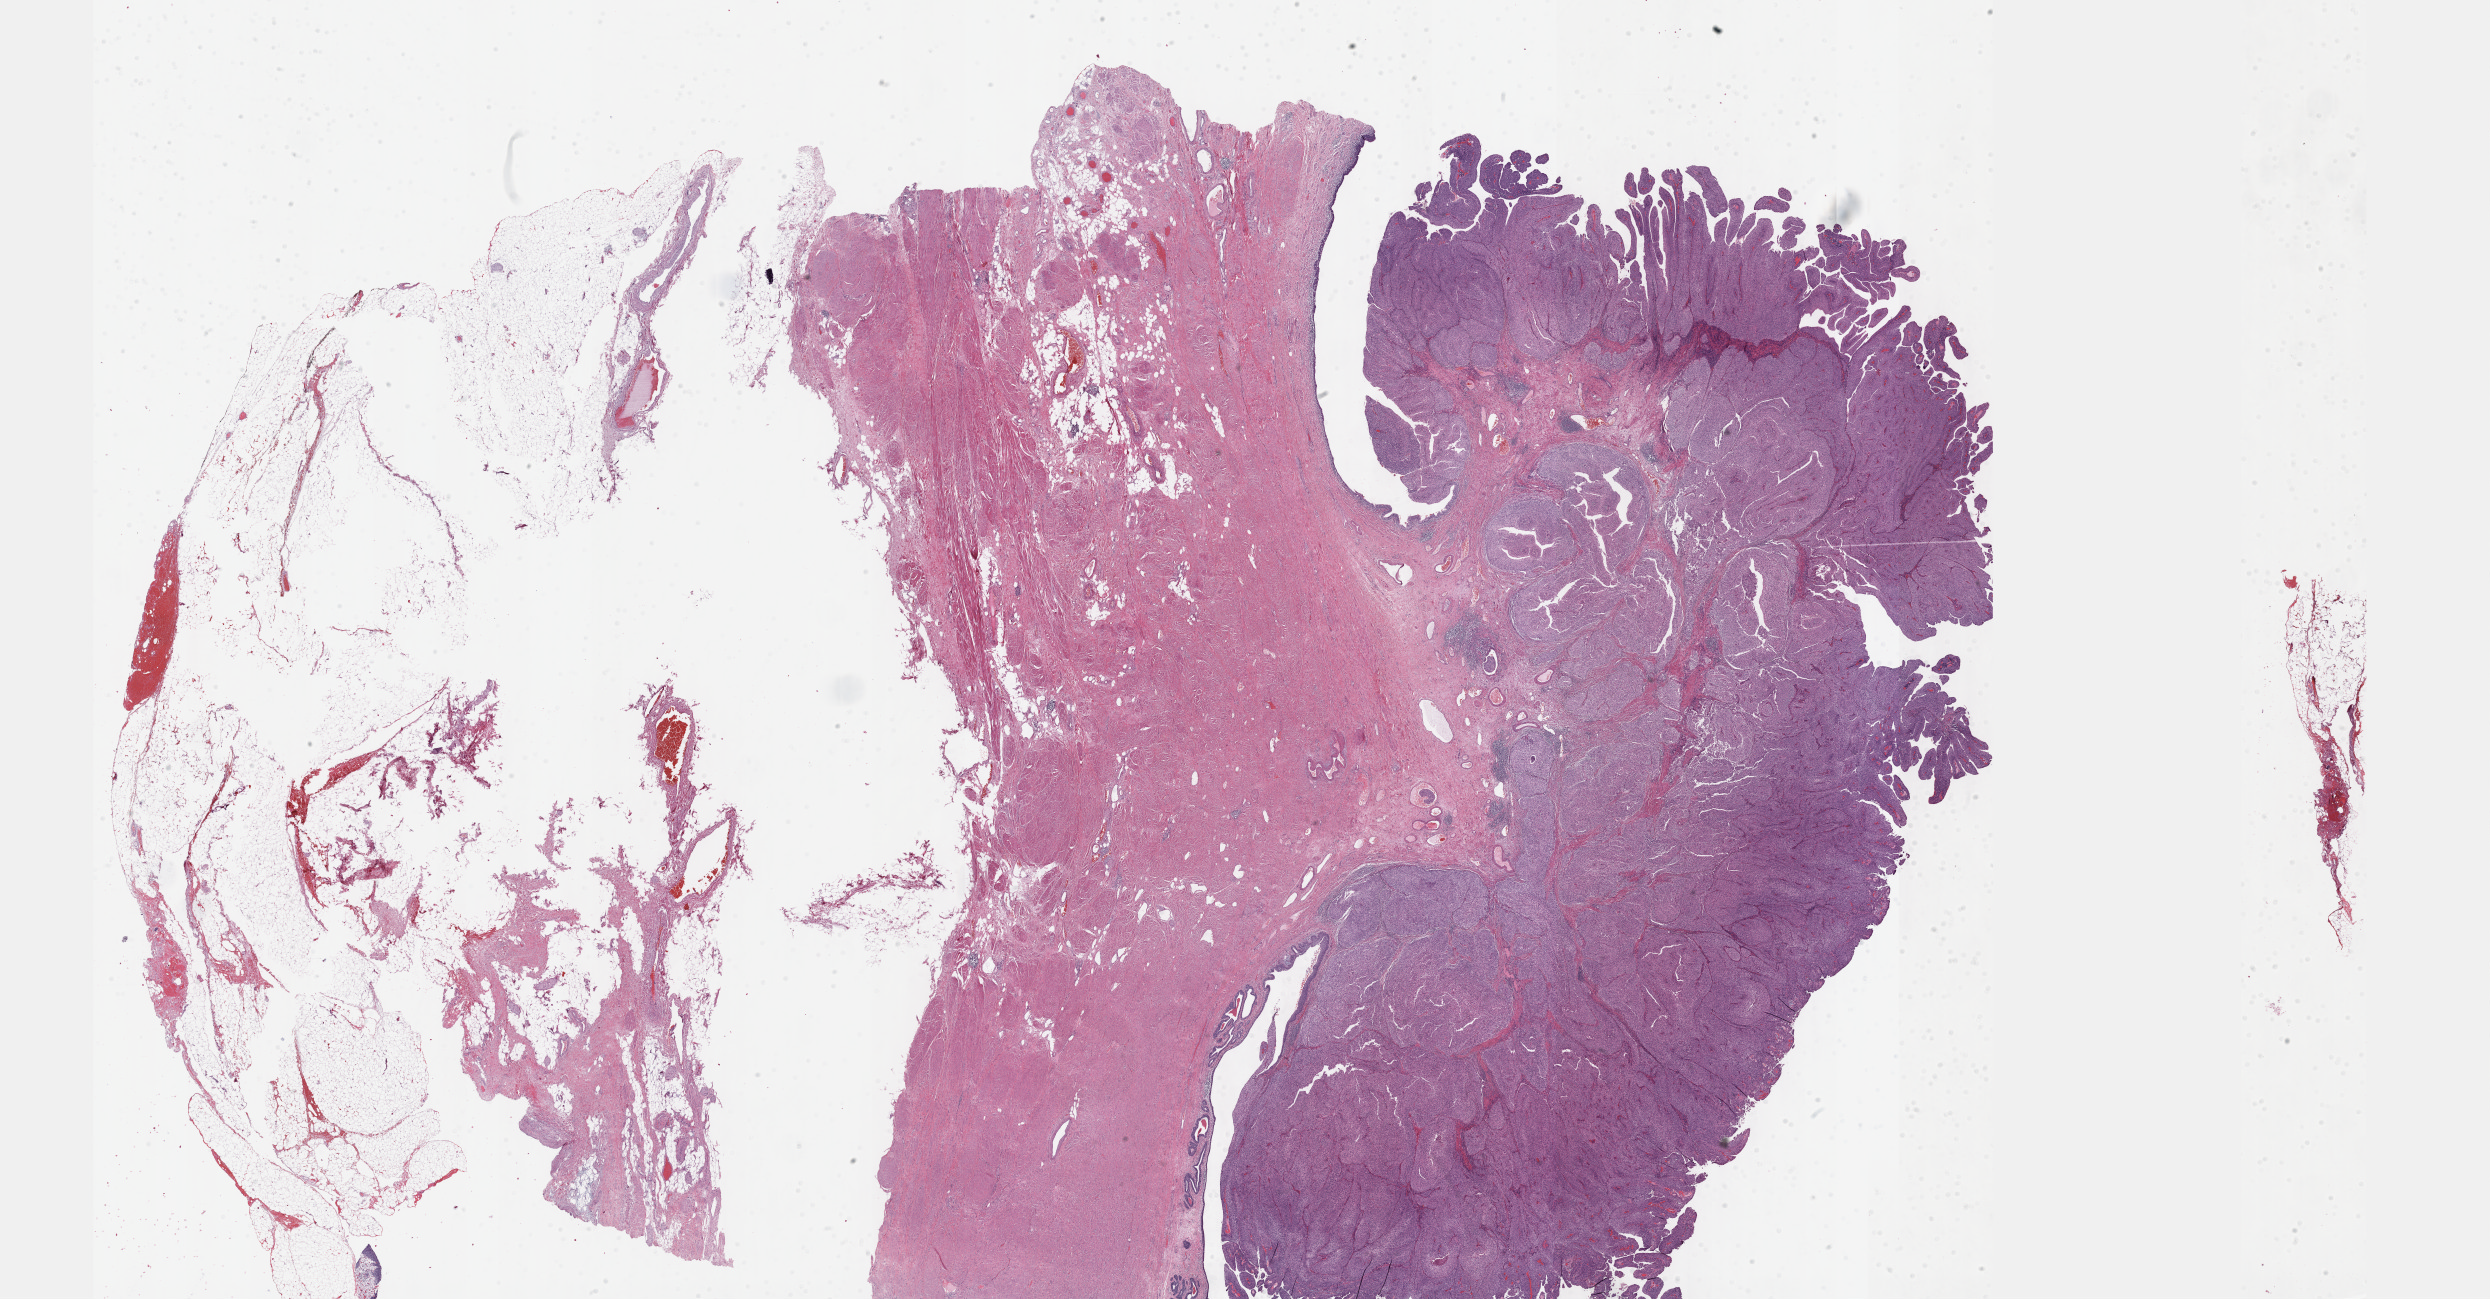
Digitized H&E-stained tissue section (whole slide) — low-resolution overview of the scanned area, about 40.2 x 21.0 mm. Formalin-fixed paraffin-embedded (FFPE) diagnostic section. Bladder, primary tumour sample. Female patient; age at initial diagnosis 69 years. Histologic grade: high grade.
AJCC pathologic stage: II (7th edition). Pathologic diagnosis: Papillary transitional cell carcinoma. TNM: T2a N0 M0.